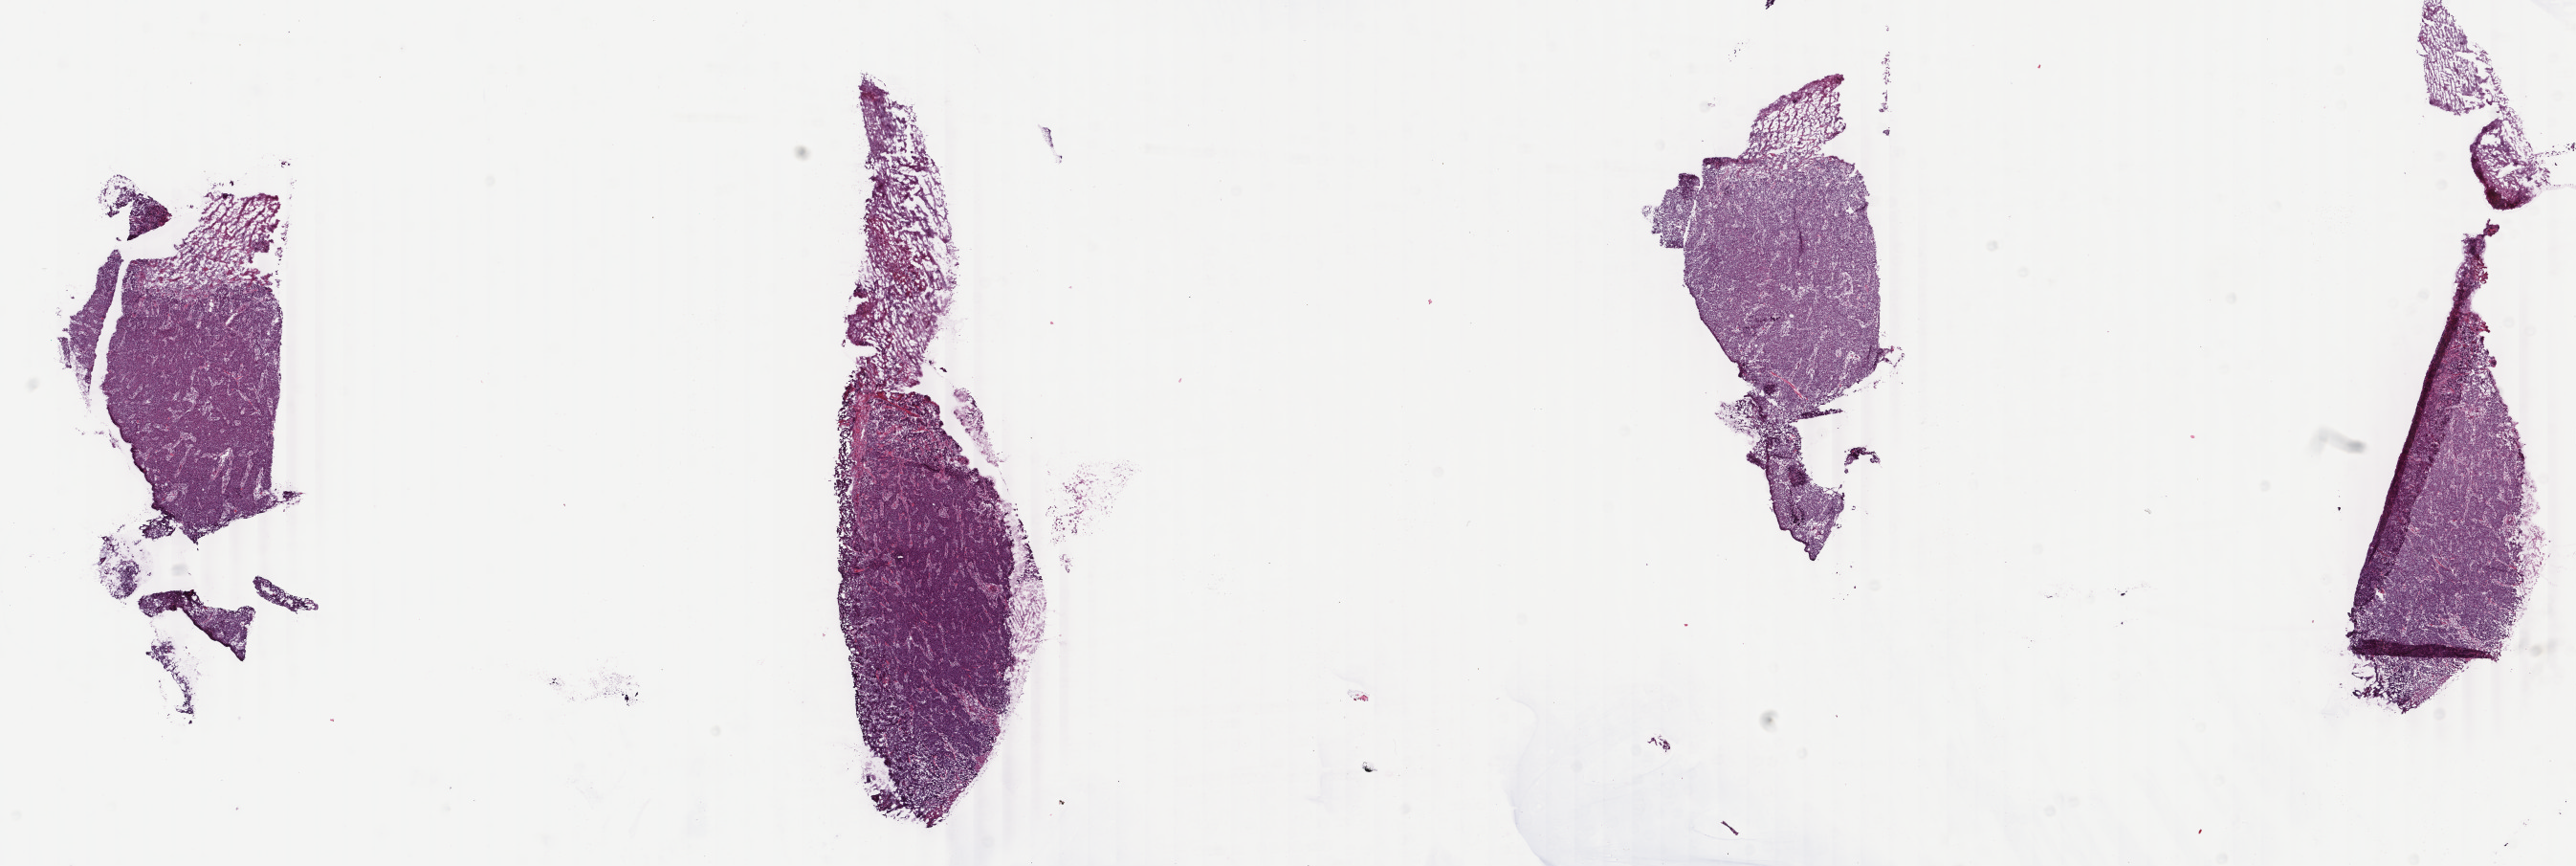
Digitized Hematoxylin and eosin (H&E) stained tissue section (whole slide) — shown as a low-resolution overview of the whole scanned area (about 21.4 x 7.2 mm, slide scanned at 40x). Frozen section from the bottom of the tissue portion. Colon, primary tumour sample. Female, age 48 years at initial diagnosis. Pathologist review of this section (percent, as recorded): tumour cells 95%, tumour nuclei 95%, normal cells 0%, stromal cells 4%, necrosis 1%. Inflammatory infiltration, as recorded: lymphocyte infiltration 1%, monocyte infiltration 1%, neutrophil infiltration 1%.
Pathologic diagnosis: Adenocarcinoma, NOS (ascending colon). Lymph nodes positive (case pathology): 0 of 16 examined. AJCC pathologic stage: II (5th edition).